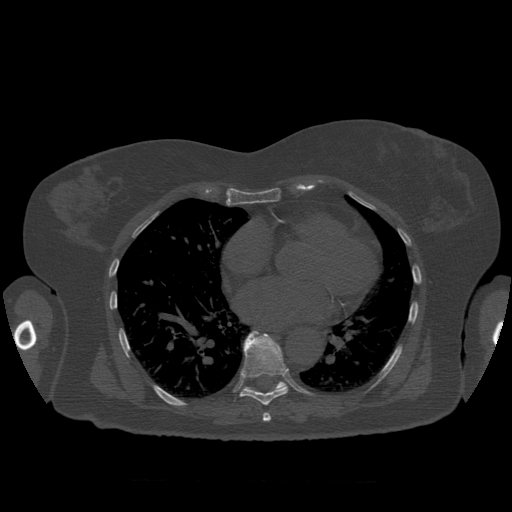
CT including the spine, one axial slice; position 374 of 399 along the scan axis; reconstruction kernel STANDARD; 120 kVp; bone window (W 1800 / L 400 HU); 512 × 512 image matrix, field of view 404 × 404 mm. Patient age 81 years. Case-level facts recorded for this patient, not image findings: primary cancer: renal; vertebrae with lytic lesions (as recorded): L1.
Annotated regions visible in this slice (semi-automatically segmented with operator editing):
- T7 vertebra: bounding box <263,413,272,422> (left, top, right, bottom; pixels)
- T8 vertebra: <240,331,289,406>
- T9 vertebra: <244,332,287,391>